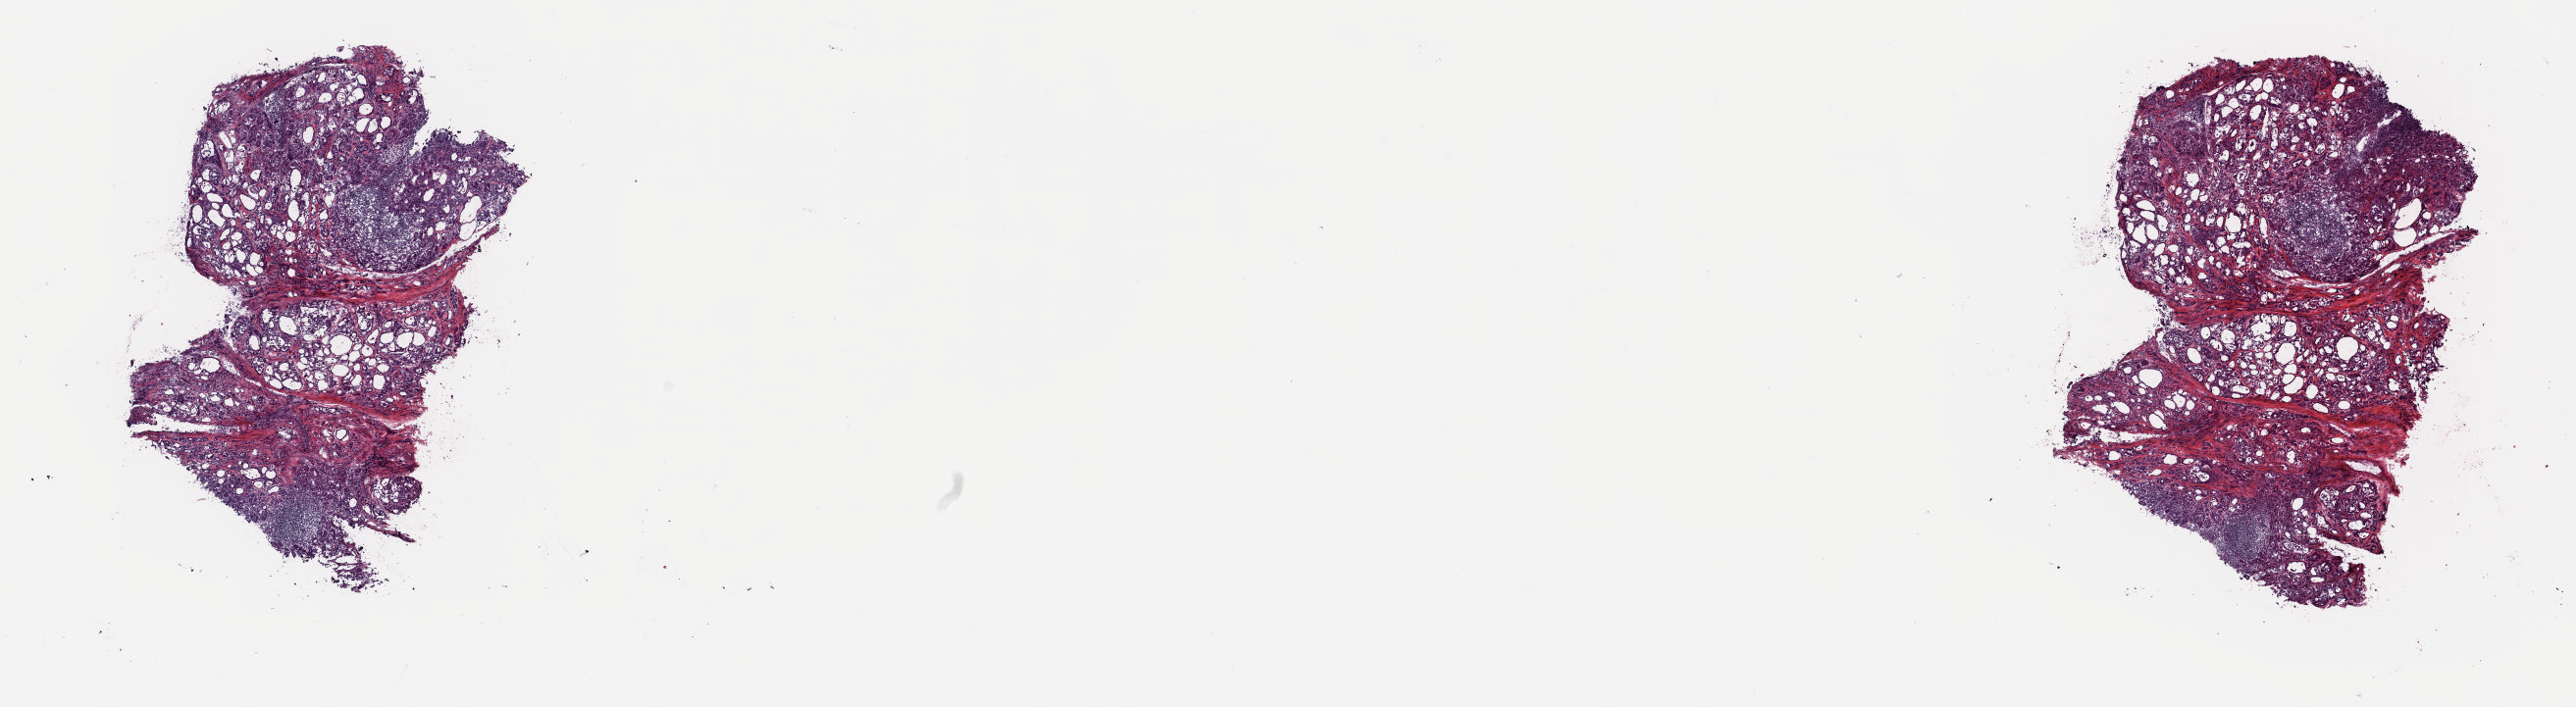
H&E whole-slide image, low-resolution overview of the scanned area, about 20.8 x 5.7 mm, frozen section from the top of the tissue portion, thyroid, solid tissue normal (non-tumour tissue) sample. Female, age 46 years at initial diagnosis. Composition of this section per pathologist review: tumour cells 0%, tumour nuclei 0%, normal cells 100%, stromal cells 0%, necrosis 0%. Inflammatory infiltration, as recorded: lymphocyte infiltration 30%, monocyte infiltration 4%, neutrophil infiltration 0%.
This section: solid tissue normal sample (biorepository sample class). Patient diagnosis: Papillary adenocarcinoma, NOS.